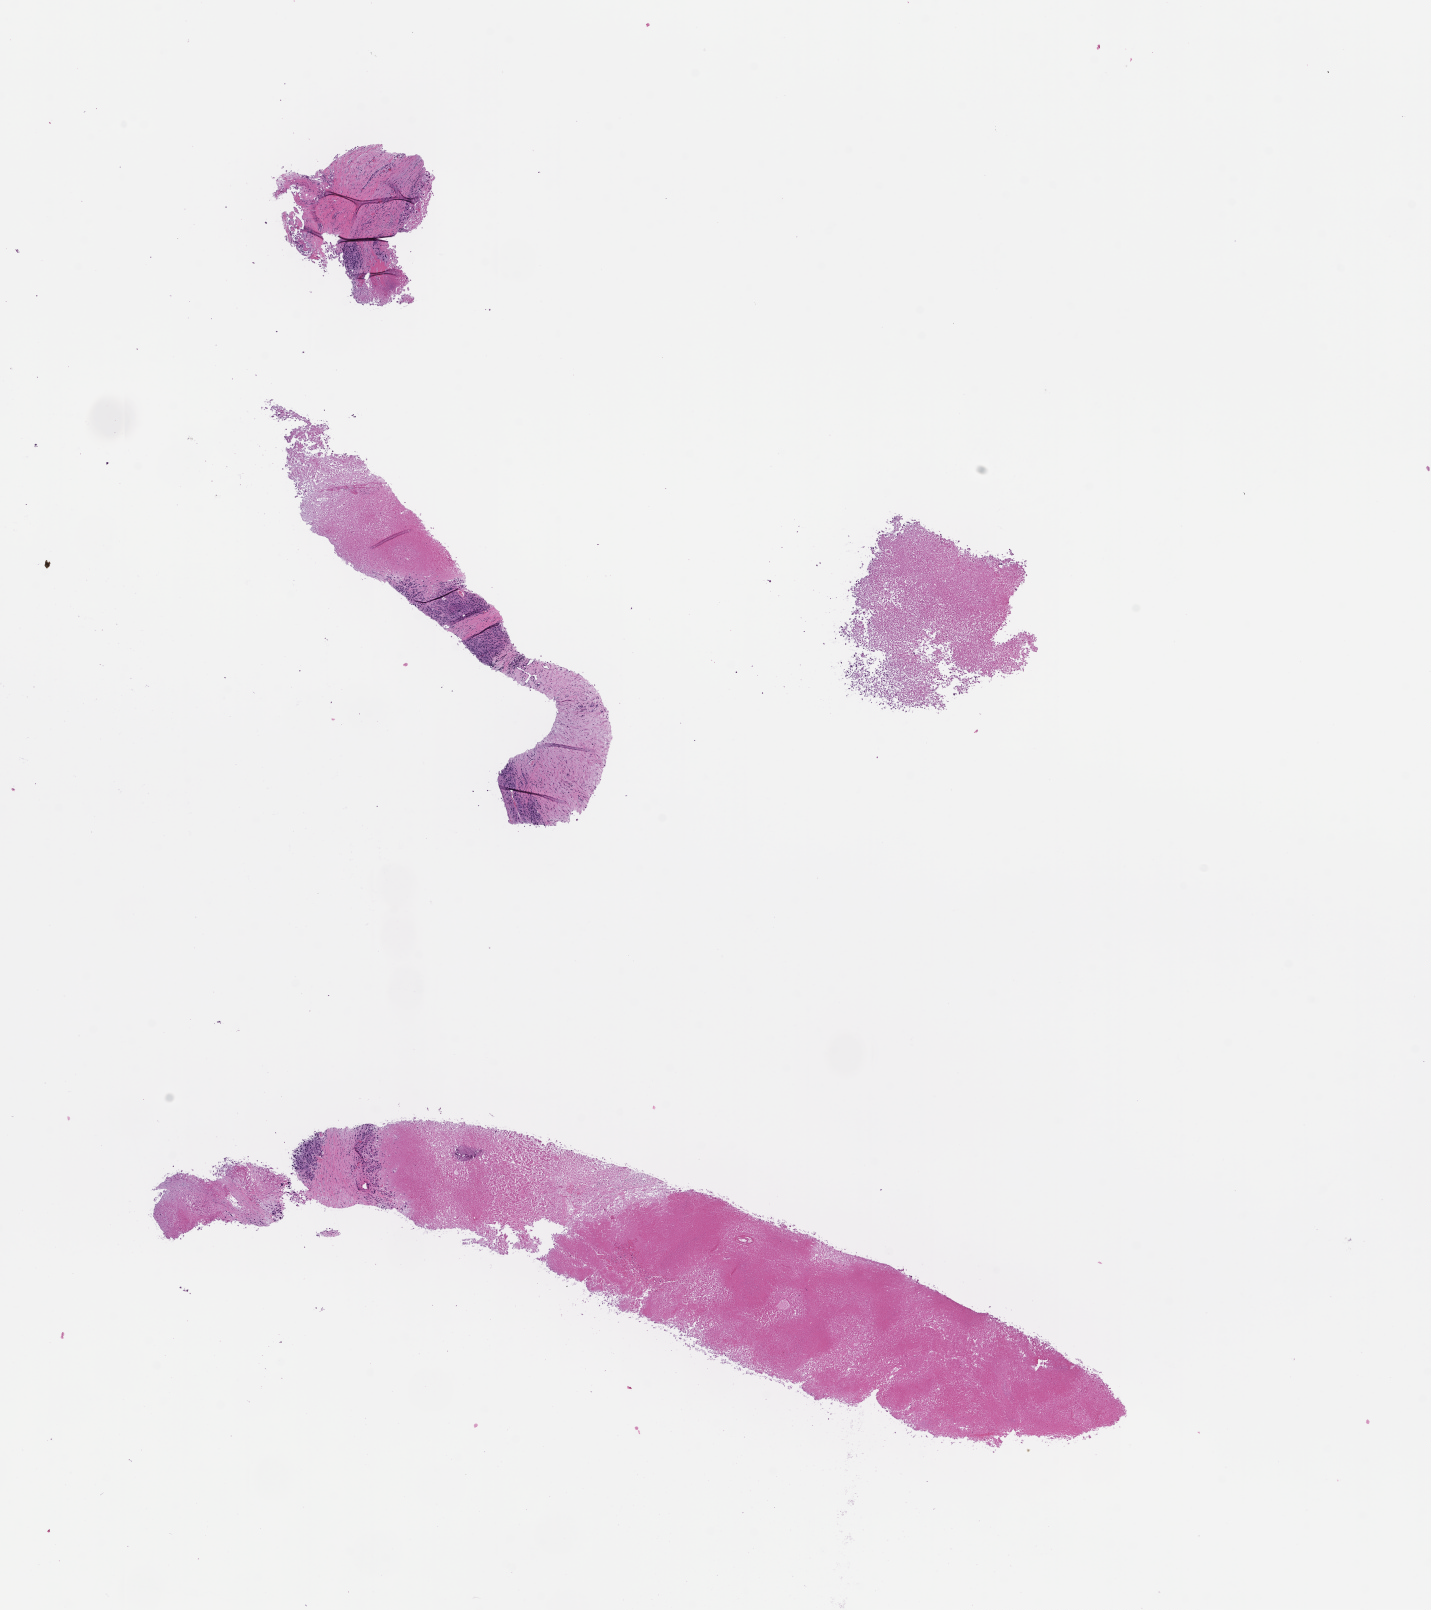
Digitized hematoxylin and eosin (H&E)-stained section — whole scanned area (about 11.6 x 13.0 mm) shown as a low-resolution overview; formalin-fixed paraffin-embedded section. Patient: female.
This section: metastatic tumor tissue. Patient diagnosis (primary): Melanoma.